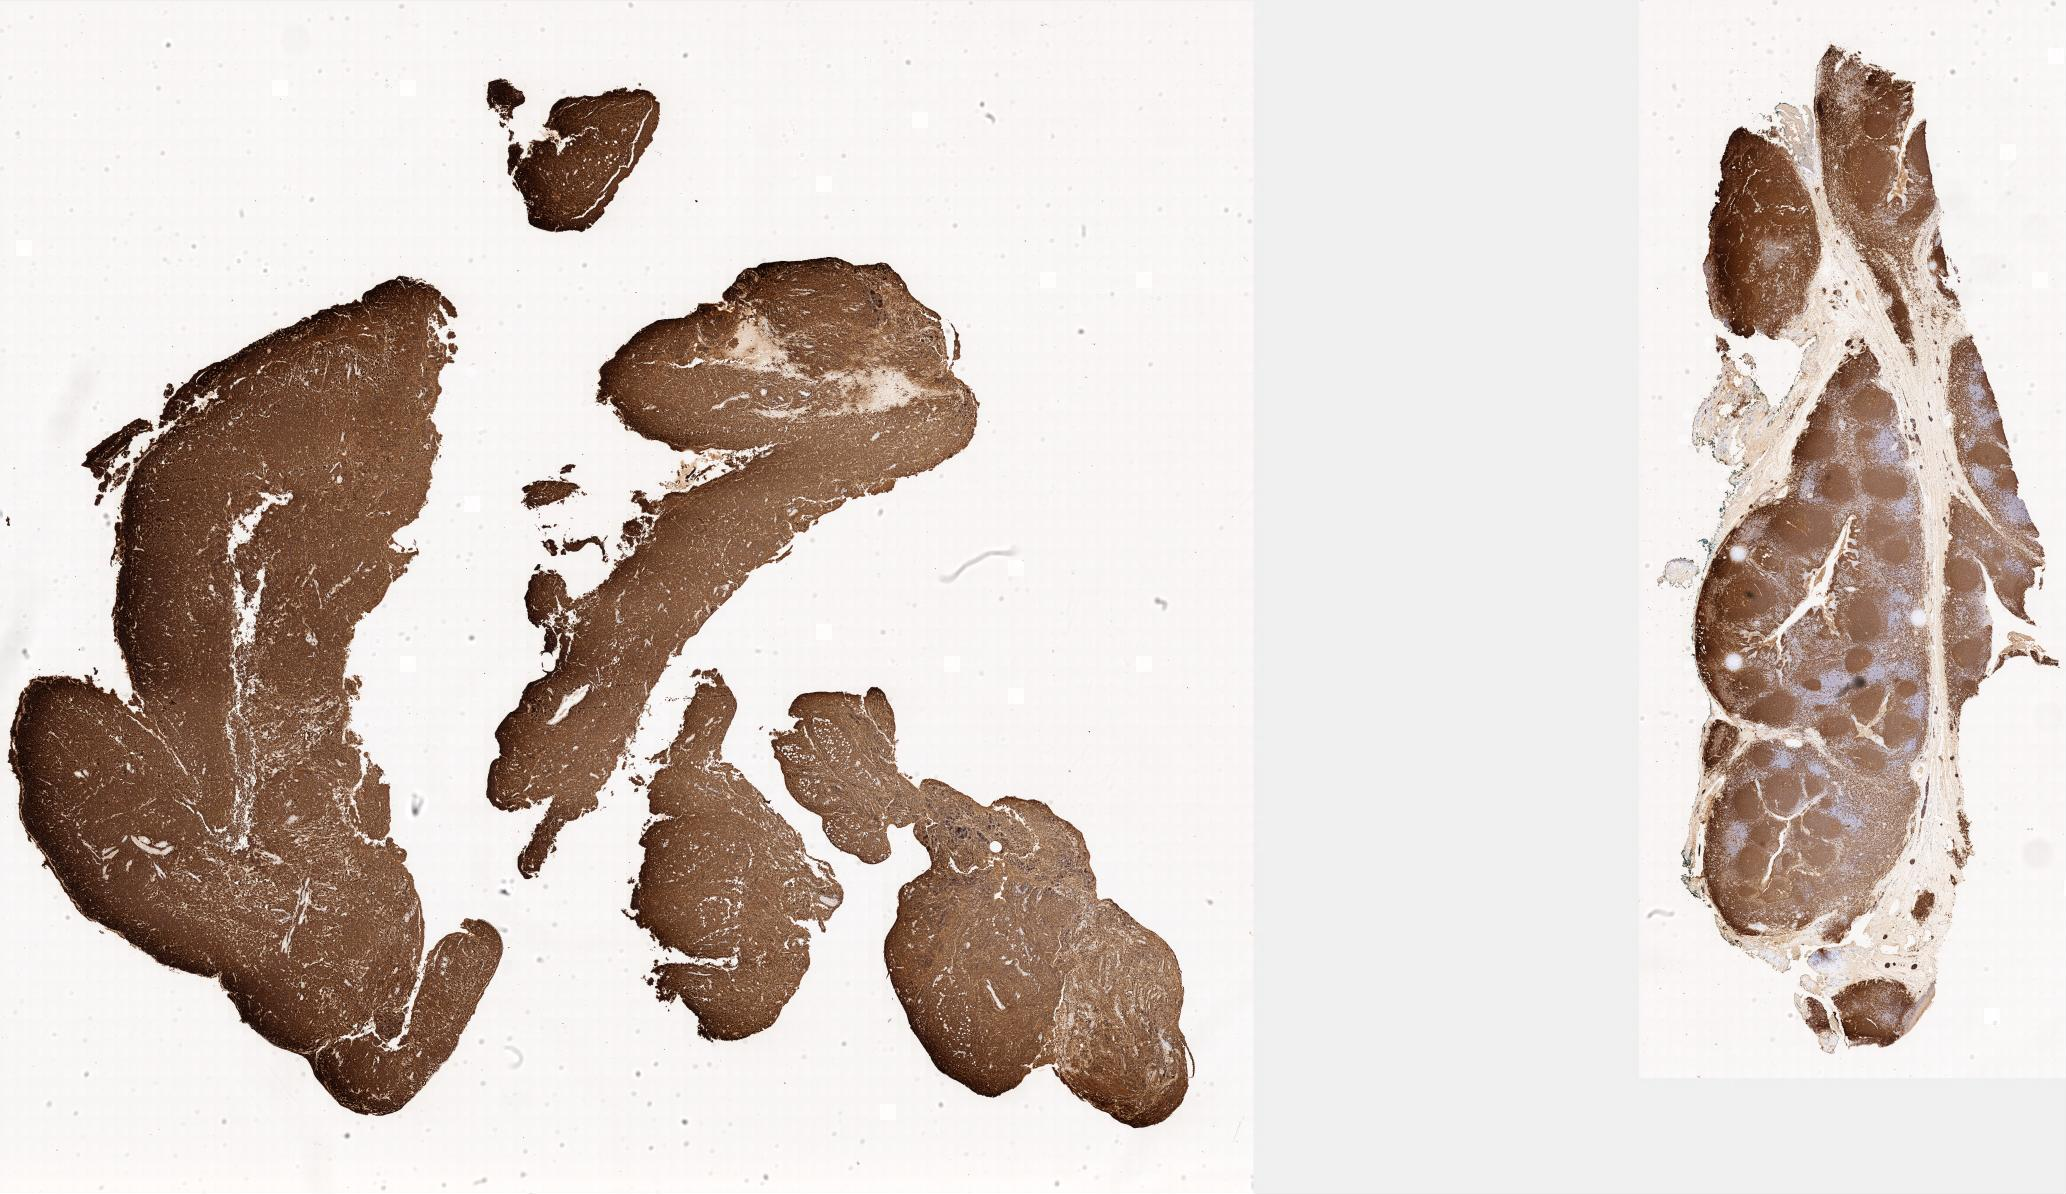
Immunohistochemistry (IHC) whole-slide image stained for CD20, low-resolution overview of the scanned area. Tumor tissue. Anatomic site: abdomen proper. Male patient; age at initial diagnosis 5 years.
Diagnosis: Burkitt lymphoma, NOS.